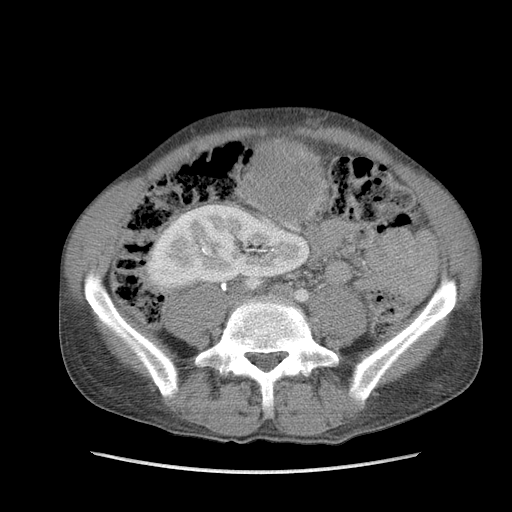
Contrast-enhanced abdominal CT, one axial slice. Position 37 of 115 along the scan axis. Soft-tissue window (W 400 / L 40 HU). 5 mm slice thickness. 512 × 512 image matrix. Male patient. From the clinical record (not read from this slice): diagnosis: adrenocortical carcinoma; tumour side: right adrenal; Ki-67 index: 13 %; stage (as recorded): 3.
Annotated regions visible in this slice (semi-automatic segmentation, software-assisted and operator-edited):
- mass: bounding box [x1, y1, x2, y2] px = [244, 138, 326, 223]